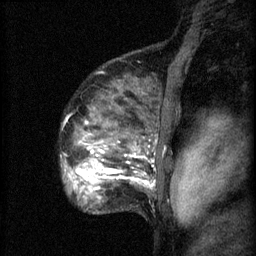
Breast MRI (dynamic contrast-enhanced), one sagittal slice; position 49 of 60 along the scan axis; 3 images stored at this slice position (order not interpretable as contrast timing); 1.5 T; TE 4.2 ms, TR 8.2 ms; 2 mm slice thickness; 256 × 256 image matrix. Patient: female, 48 years.
Outlined on this slice (semi-automatically segmented with operator editing):
- analysis volume of interest (the breast-tissue region the enhancement analysis was run in; not a lesion): box from (x=61, y=138) to (x=153, y=201) px
- tumour enhancement mask (voxels above the 70 % enhancement threshold inside the analysis volume of interest): (x=68, y=160)–(x=103, y=193)